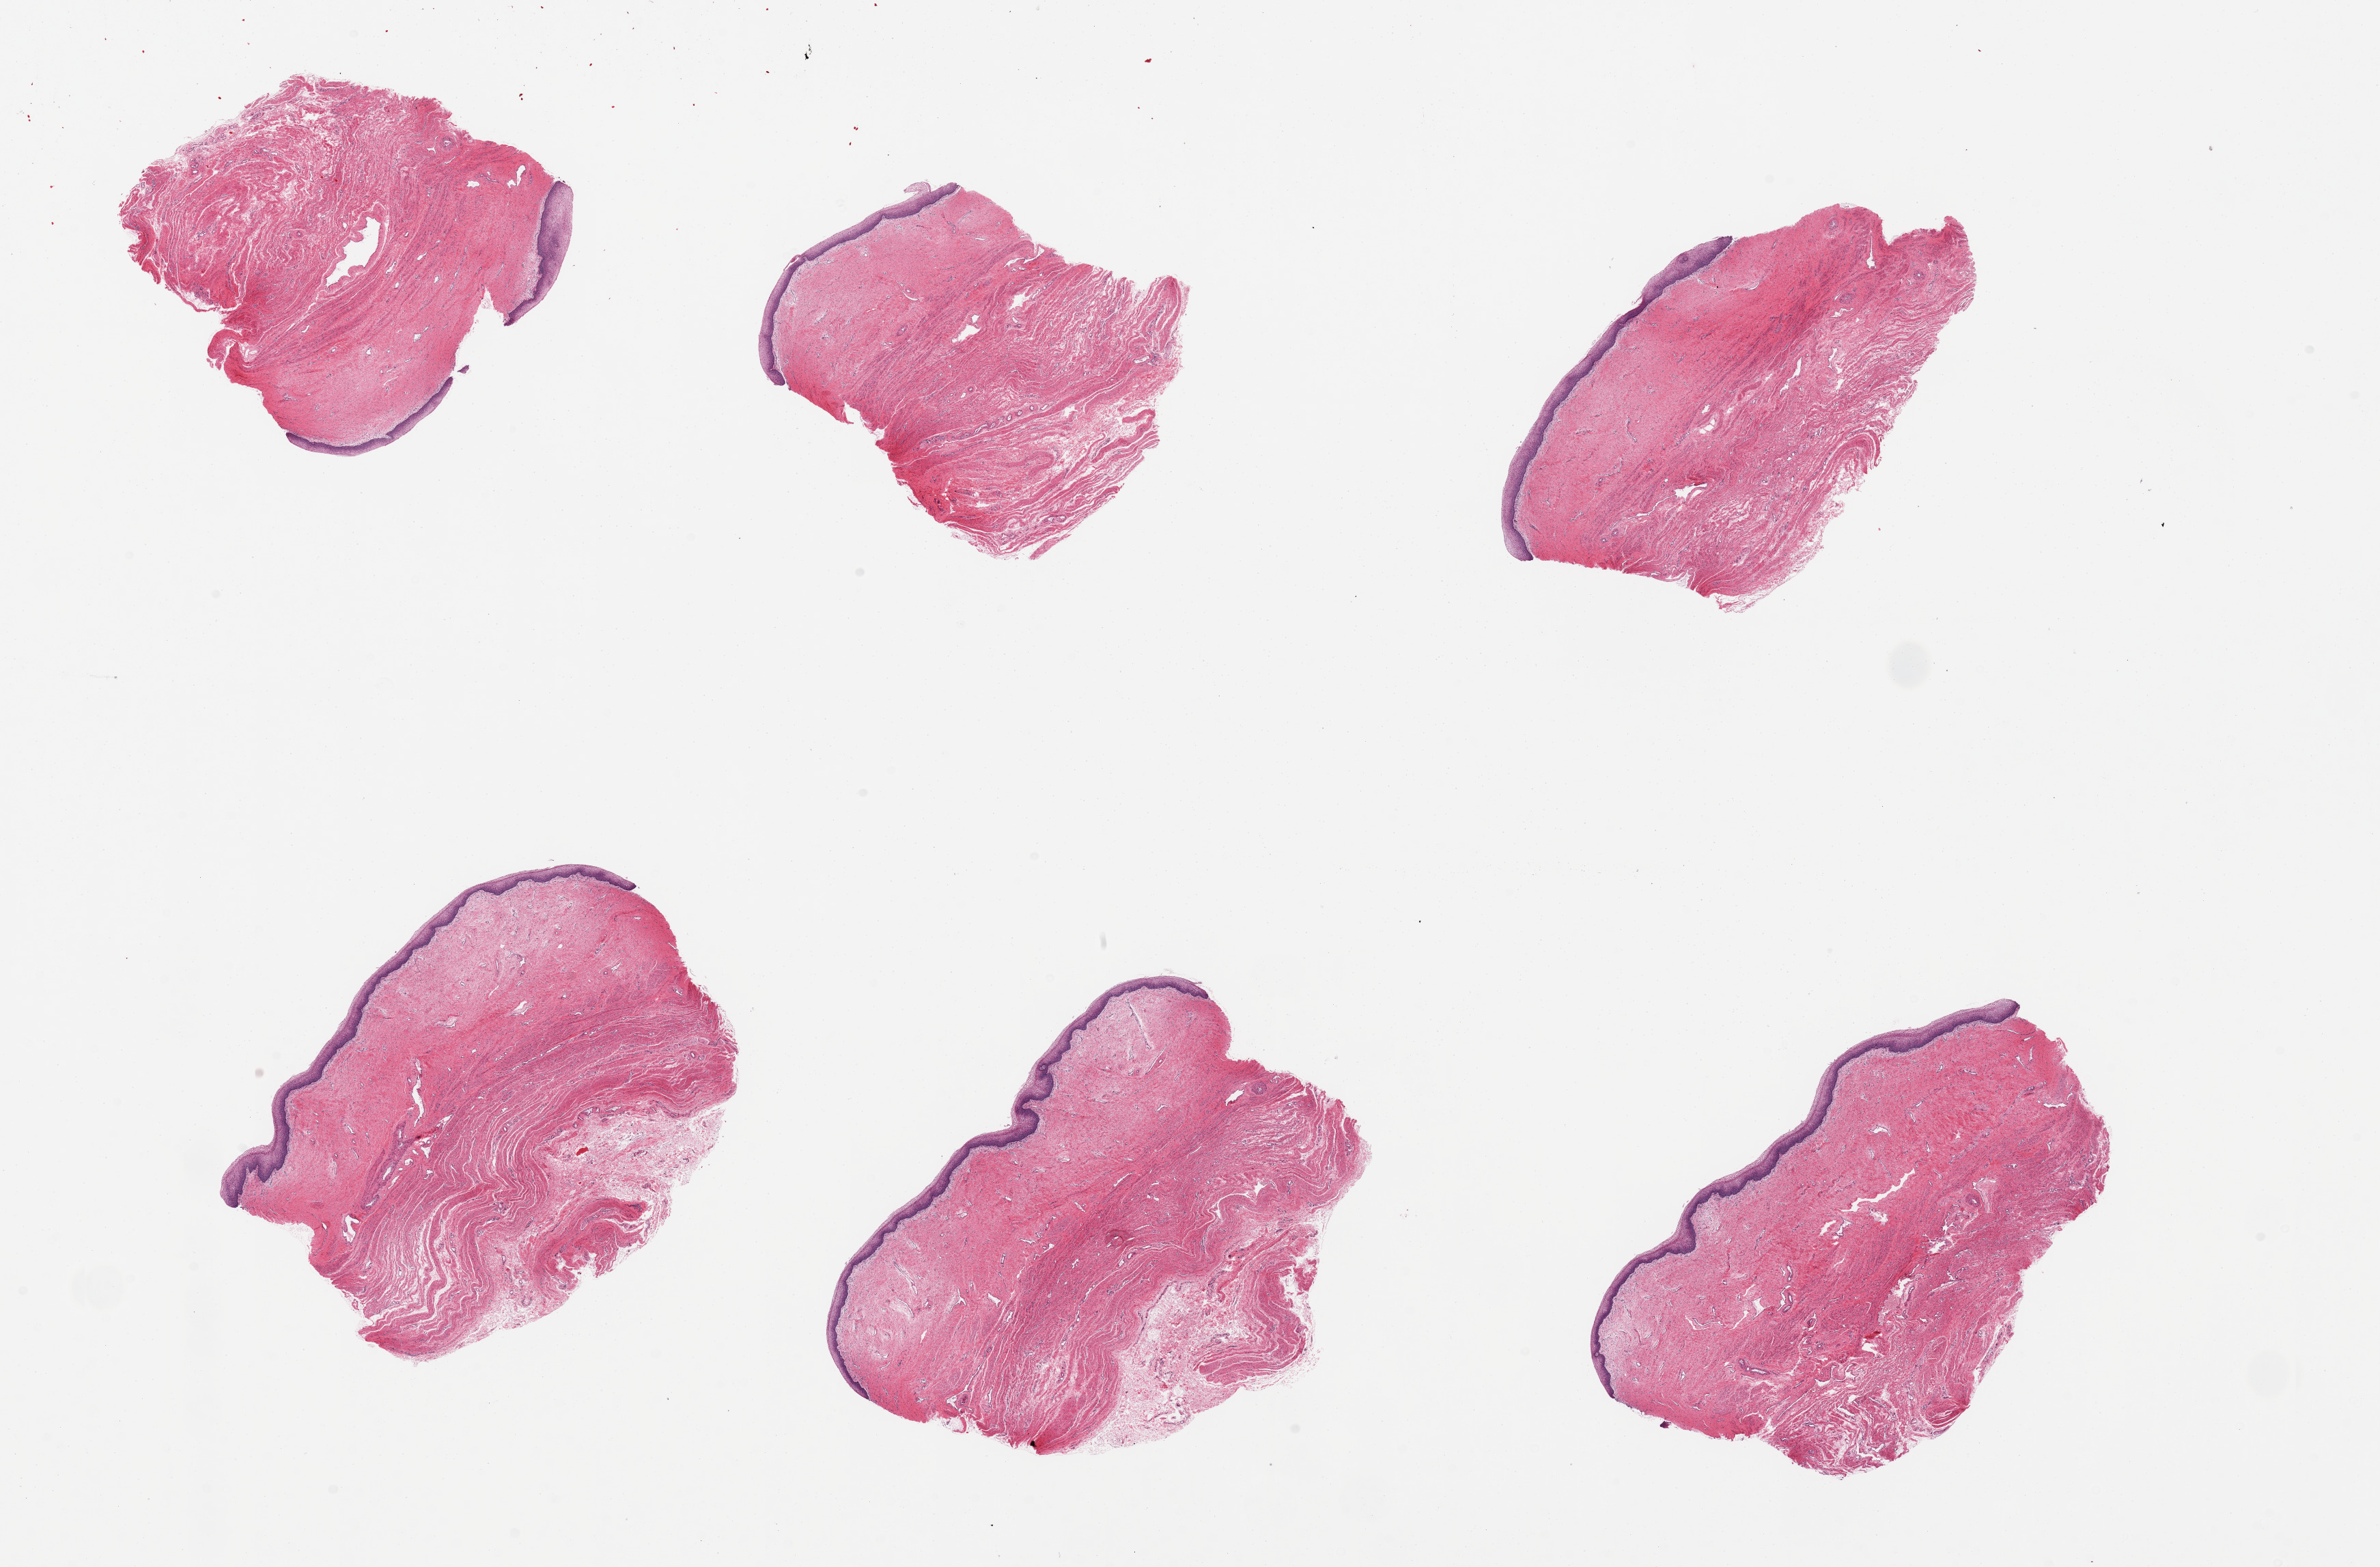
Haematoxylin and eosin whole-slide image — shown as a low-resolution overview of the whole scanned area (about 27.6 x 18.1 mm, slide scanned at 20x); PAXgene-fixed paraffin-embedded (PFPE) section; target tissue: vagina; tissue donor sample. Donor sex: female.
* reviewer comment on this tissue sample: 6 pieces